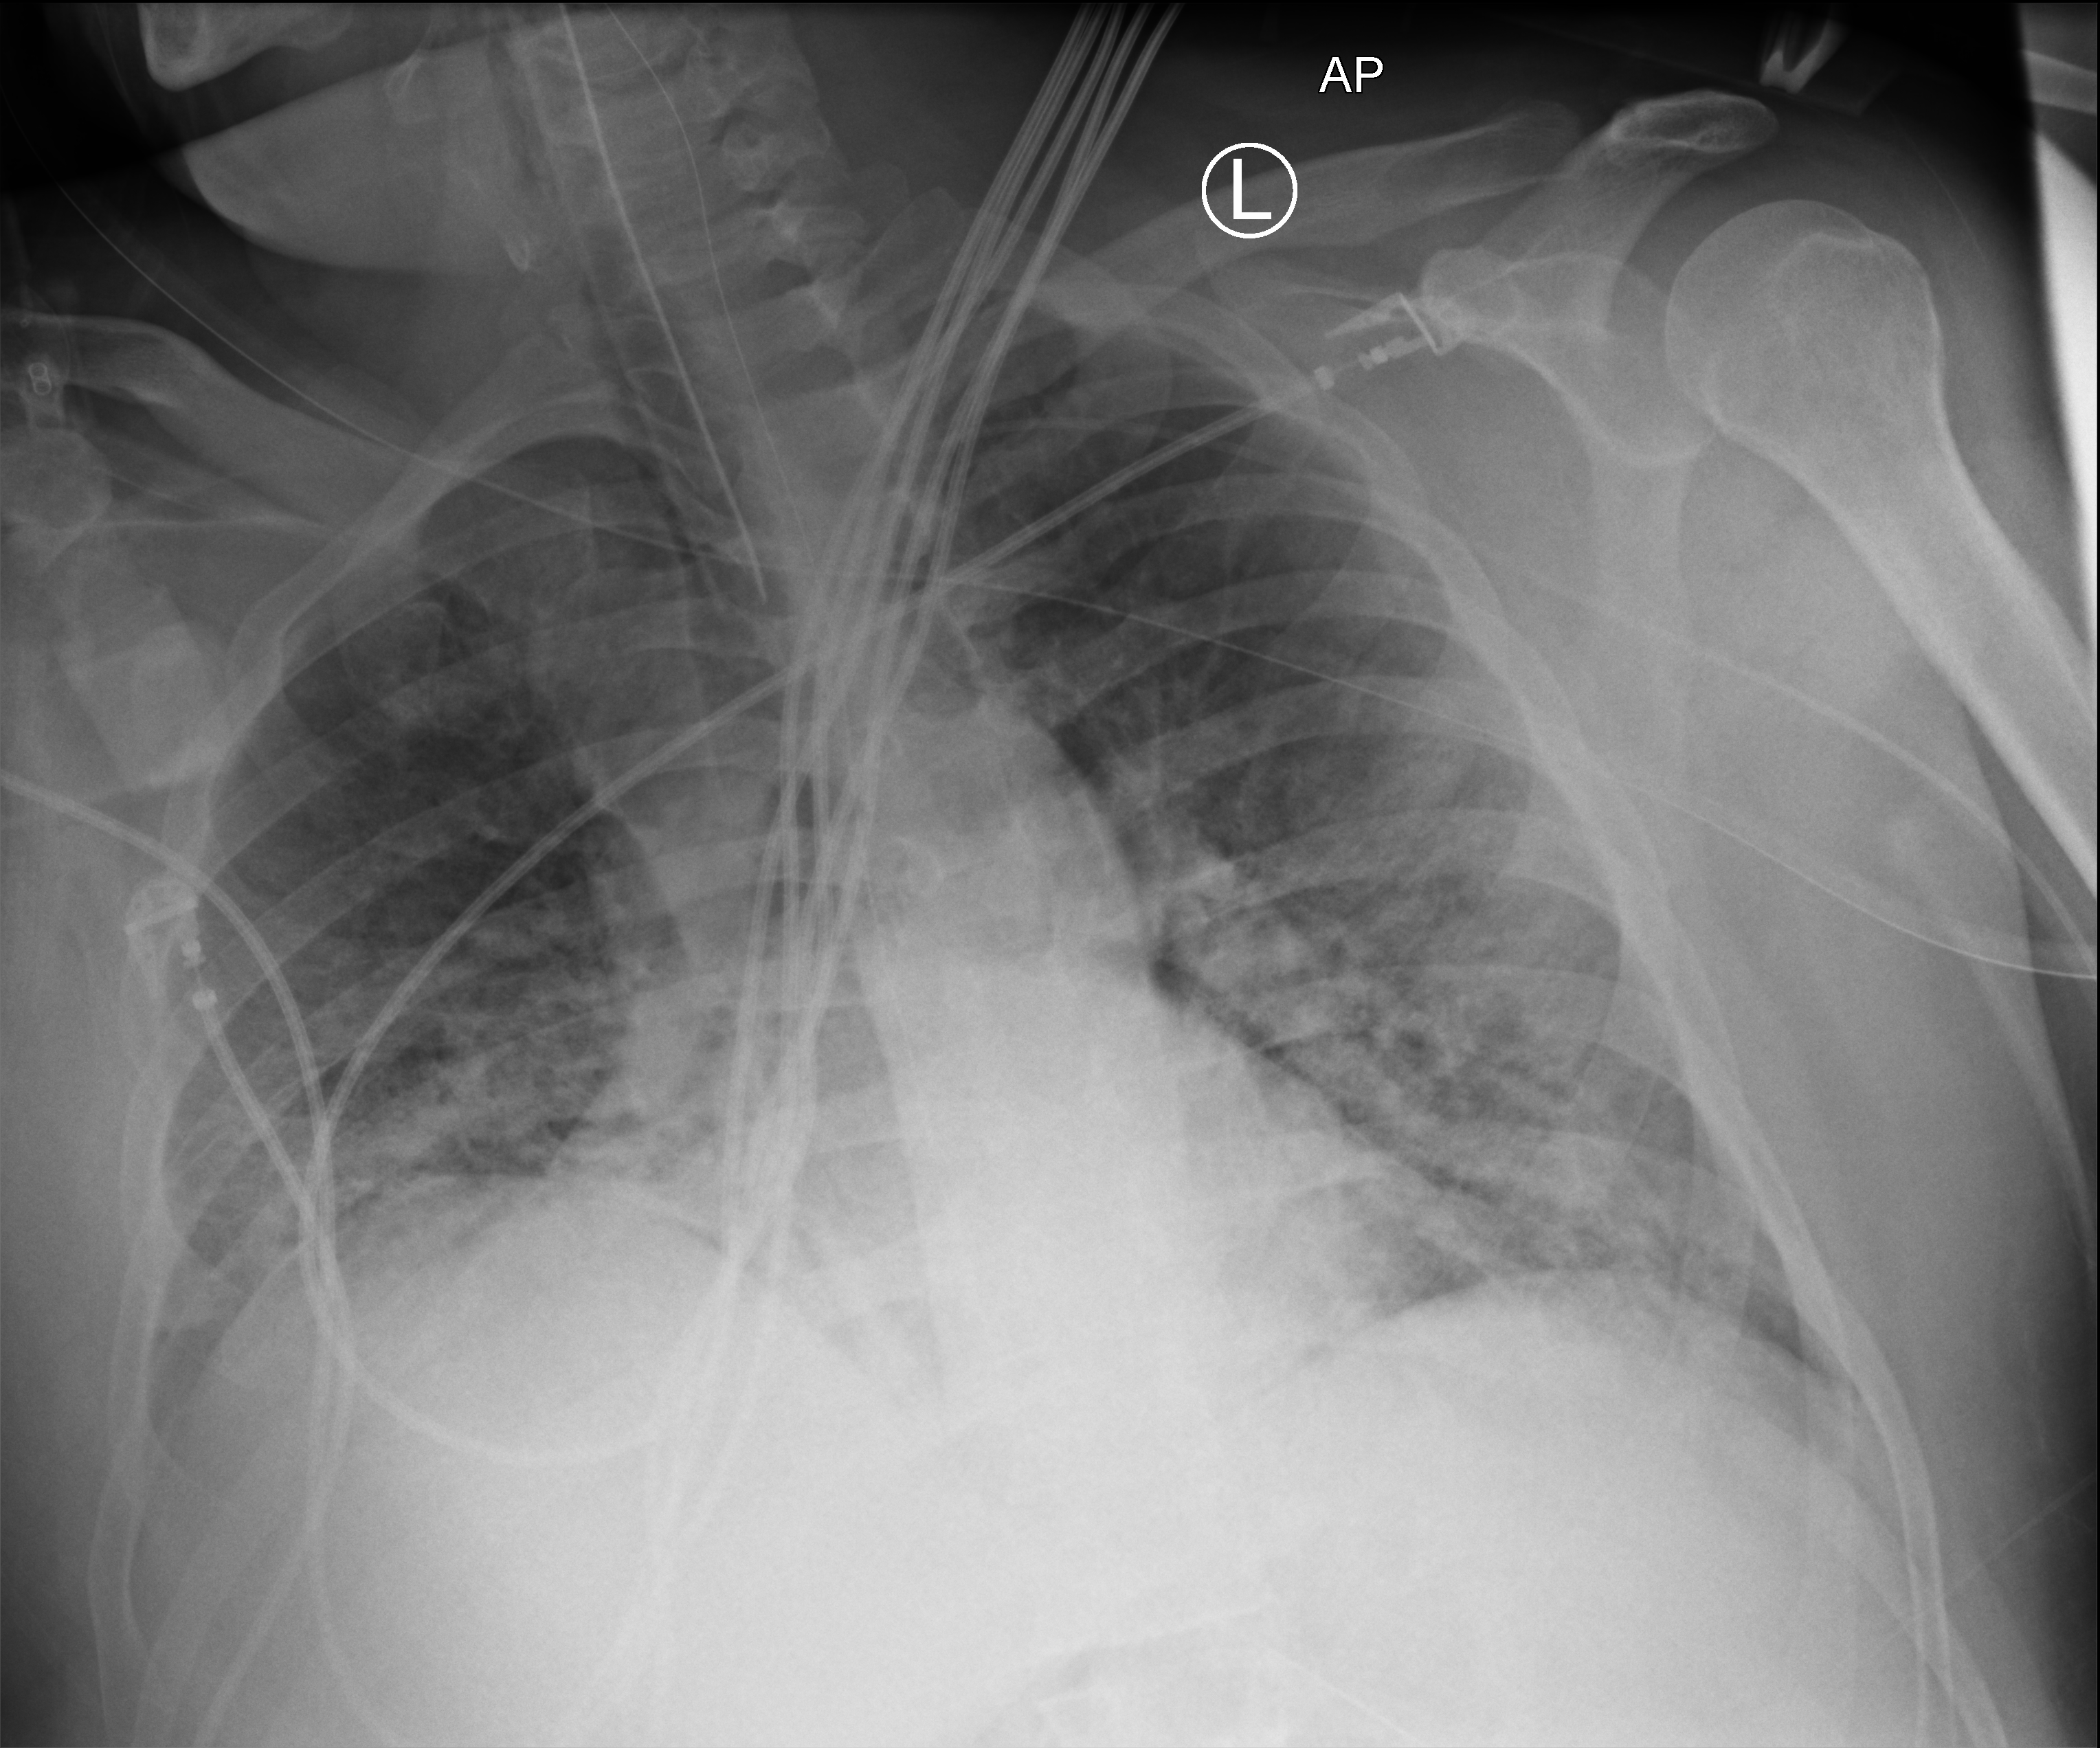
Bedside chest radiograph (computed radiography); anteroposterior (AP) projection. Patient hospitalised with COVID-19; male, aged 18–59 years.
Admission-level facts for this patient (not findings on this image; timing relative to this image not recorded): diabetes (admission record): no.